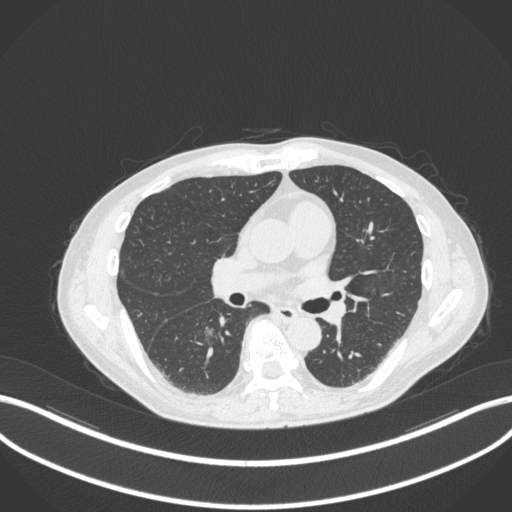
Chest CT, one axial slice; position 174 of 324 along the scan axis; reconstruction kernel B31f; lung window (W 1500 / L -600 HU); 512 × 512 image matrix. Male patient, age 61 years. From the clinical record (not read from this slice): clinical TNM (as recorded): T1c N0 M0.
Outlined on this slice (rectangle marked by the reading radiologist):
- lung tumour (recorded histology: adenocarcinoma): bounding box <198,322,218,343> (left, top, right, bottom; pixels)